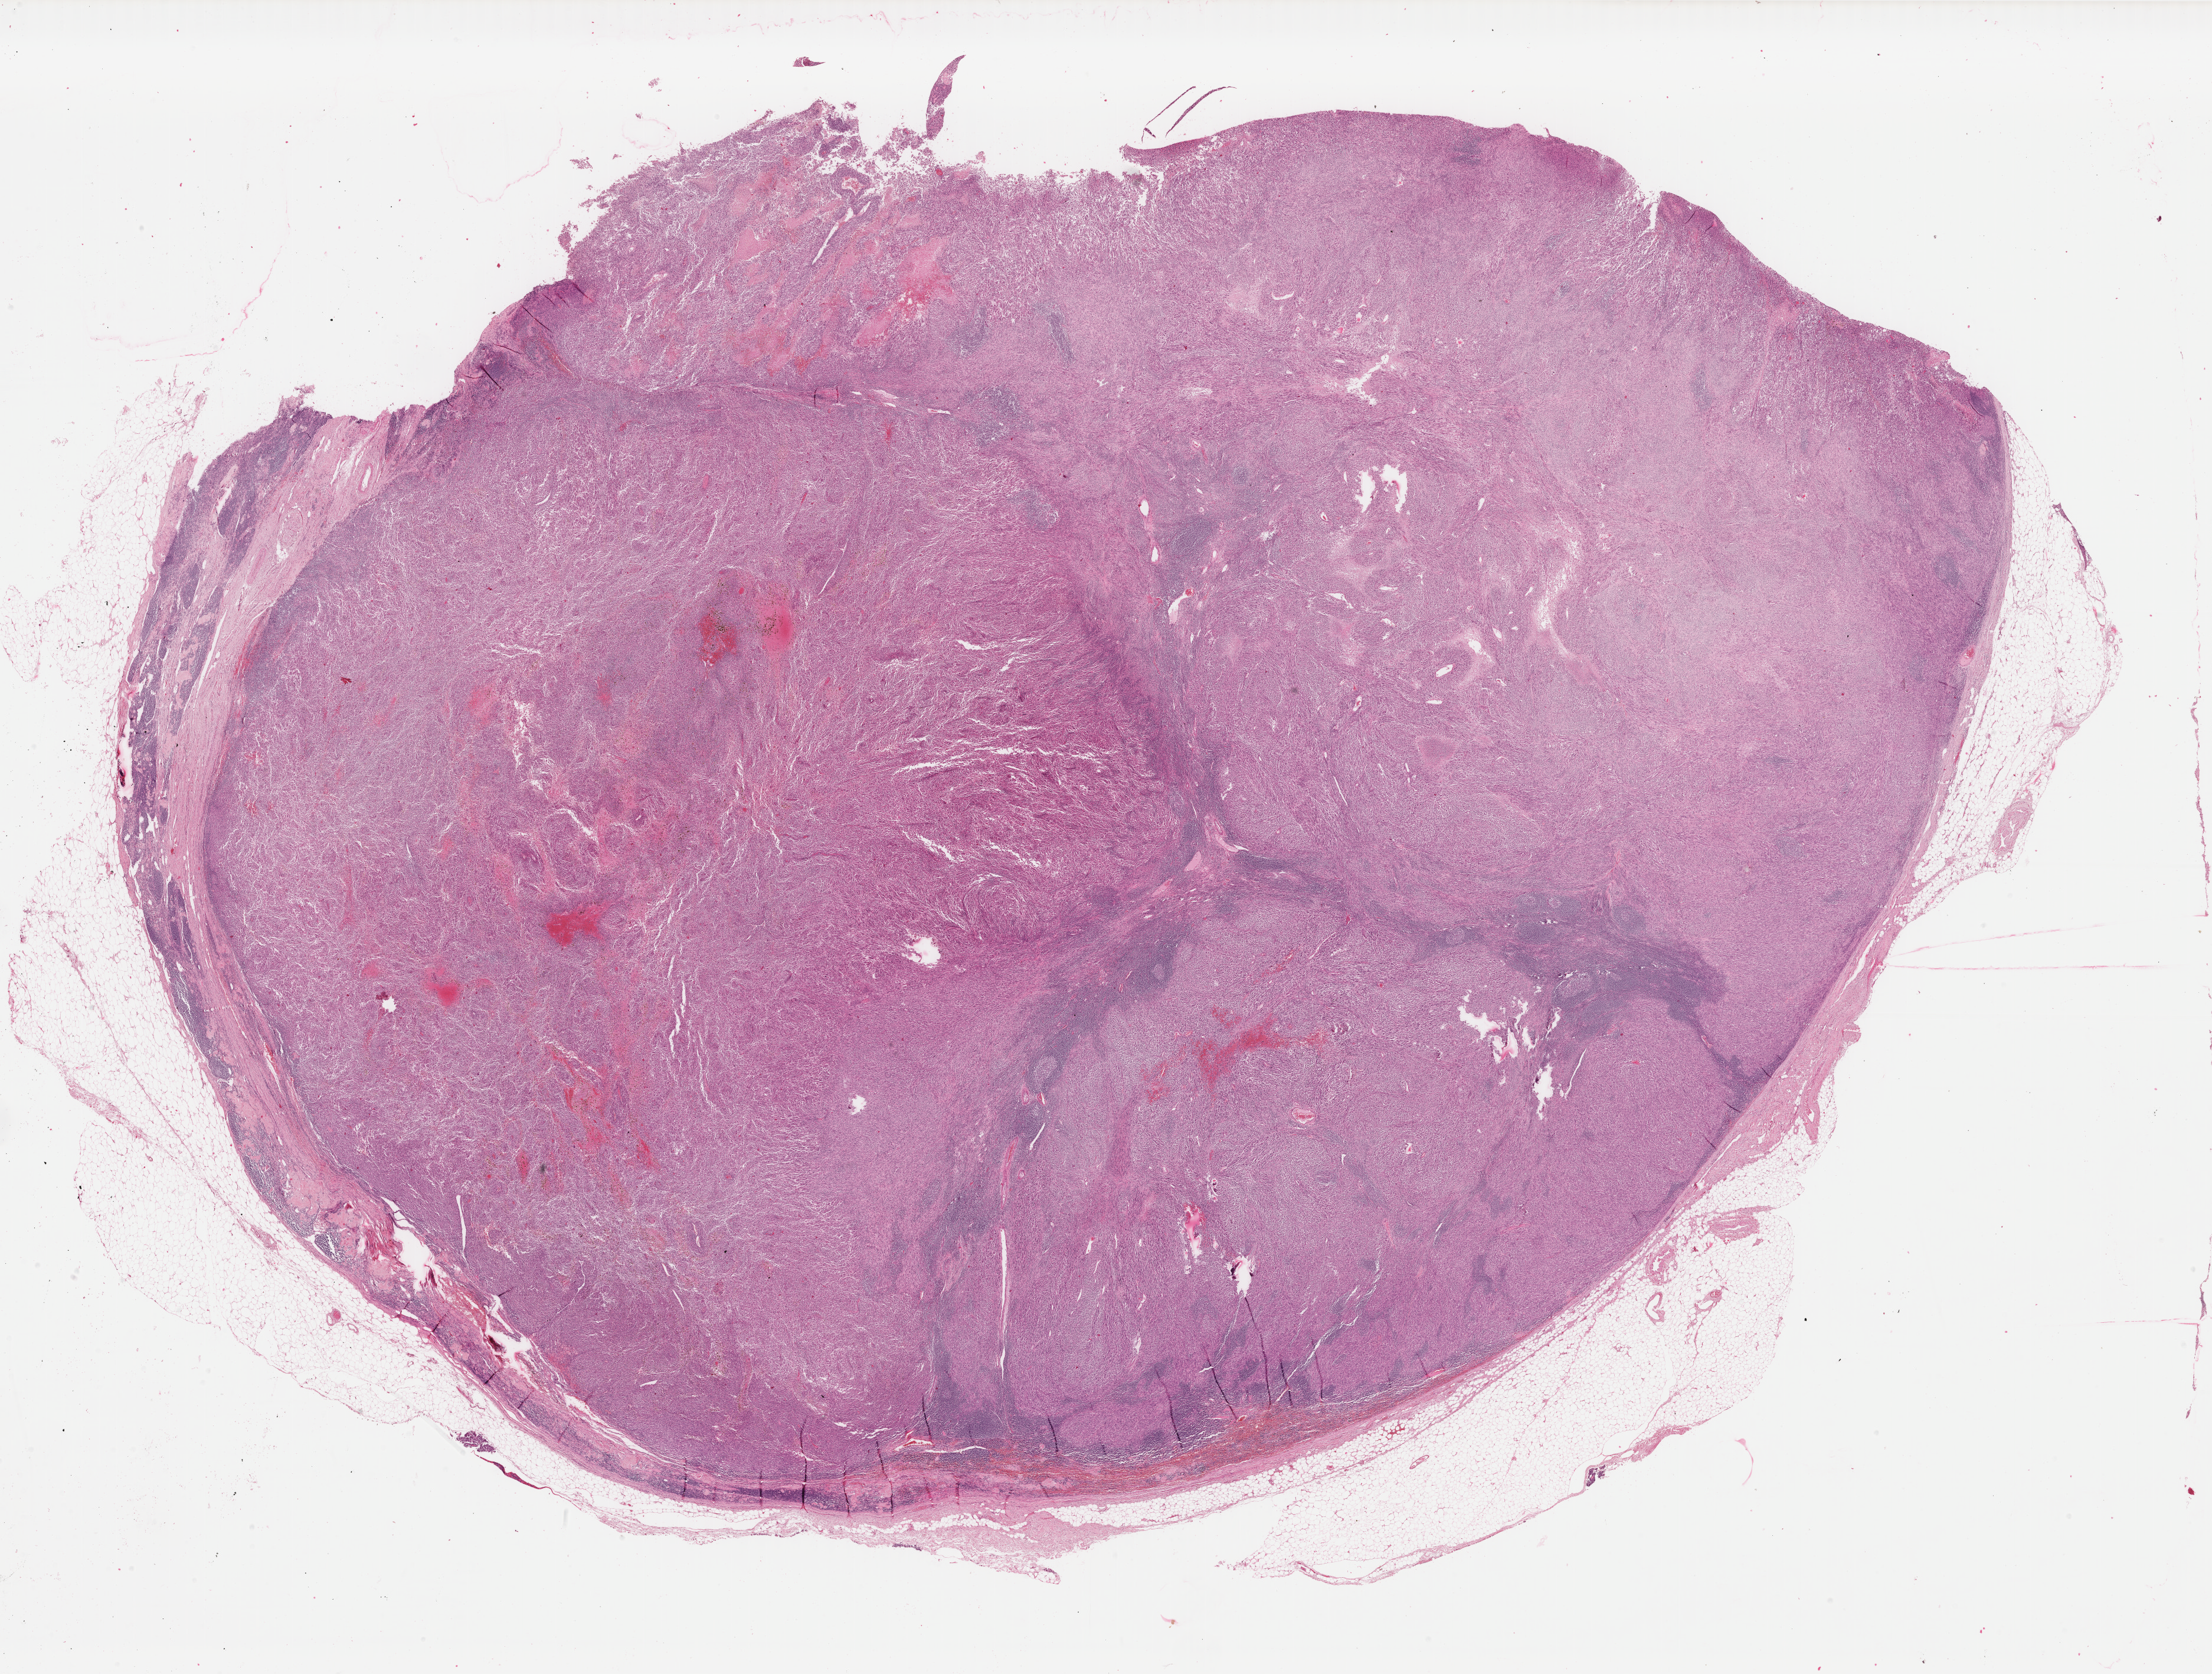
Whole-slide histology image, H&E — whole scanned area (about 29.7 x 22.5 mm, from a 40x scan) shown as a low-resolution overview. Formalin-fixed paraffin-embedded (FFPE) diagnostic section. Primary tumour sample from the skin. Female patient; age at initial diagnosis 82 years.
Pathologic diagnosis: Malignant melanoma, NOS.